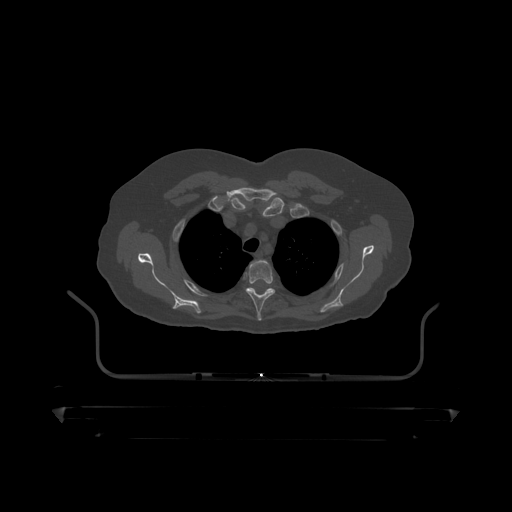
CT including the spine, one axial slice; slice 355 of 390 in the series (ordered by position); reconstruction kernel STANDARD; 120 kVp; bone window (W 1800 / L 400 HU); 1.25 mm slice thickness; 512 × 512 image matrix, field of view 650 × 650 mm. Patient: male, 60 years. From the clinical record (not read from this slice): primary cancer: prostate.
Structures marked on this image (semi-automatically segmented with operator editing):
- T3 vertebra: box from (x=246, y=260) to (x=275, y=319) px
- T4 vertebra: (x=247, y=288)–(x=286, y=304)